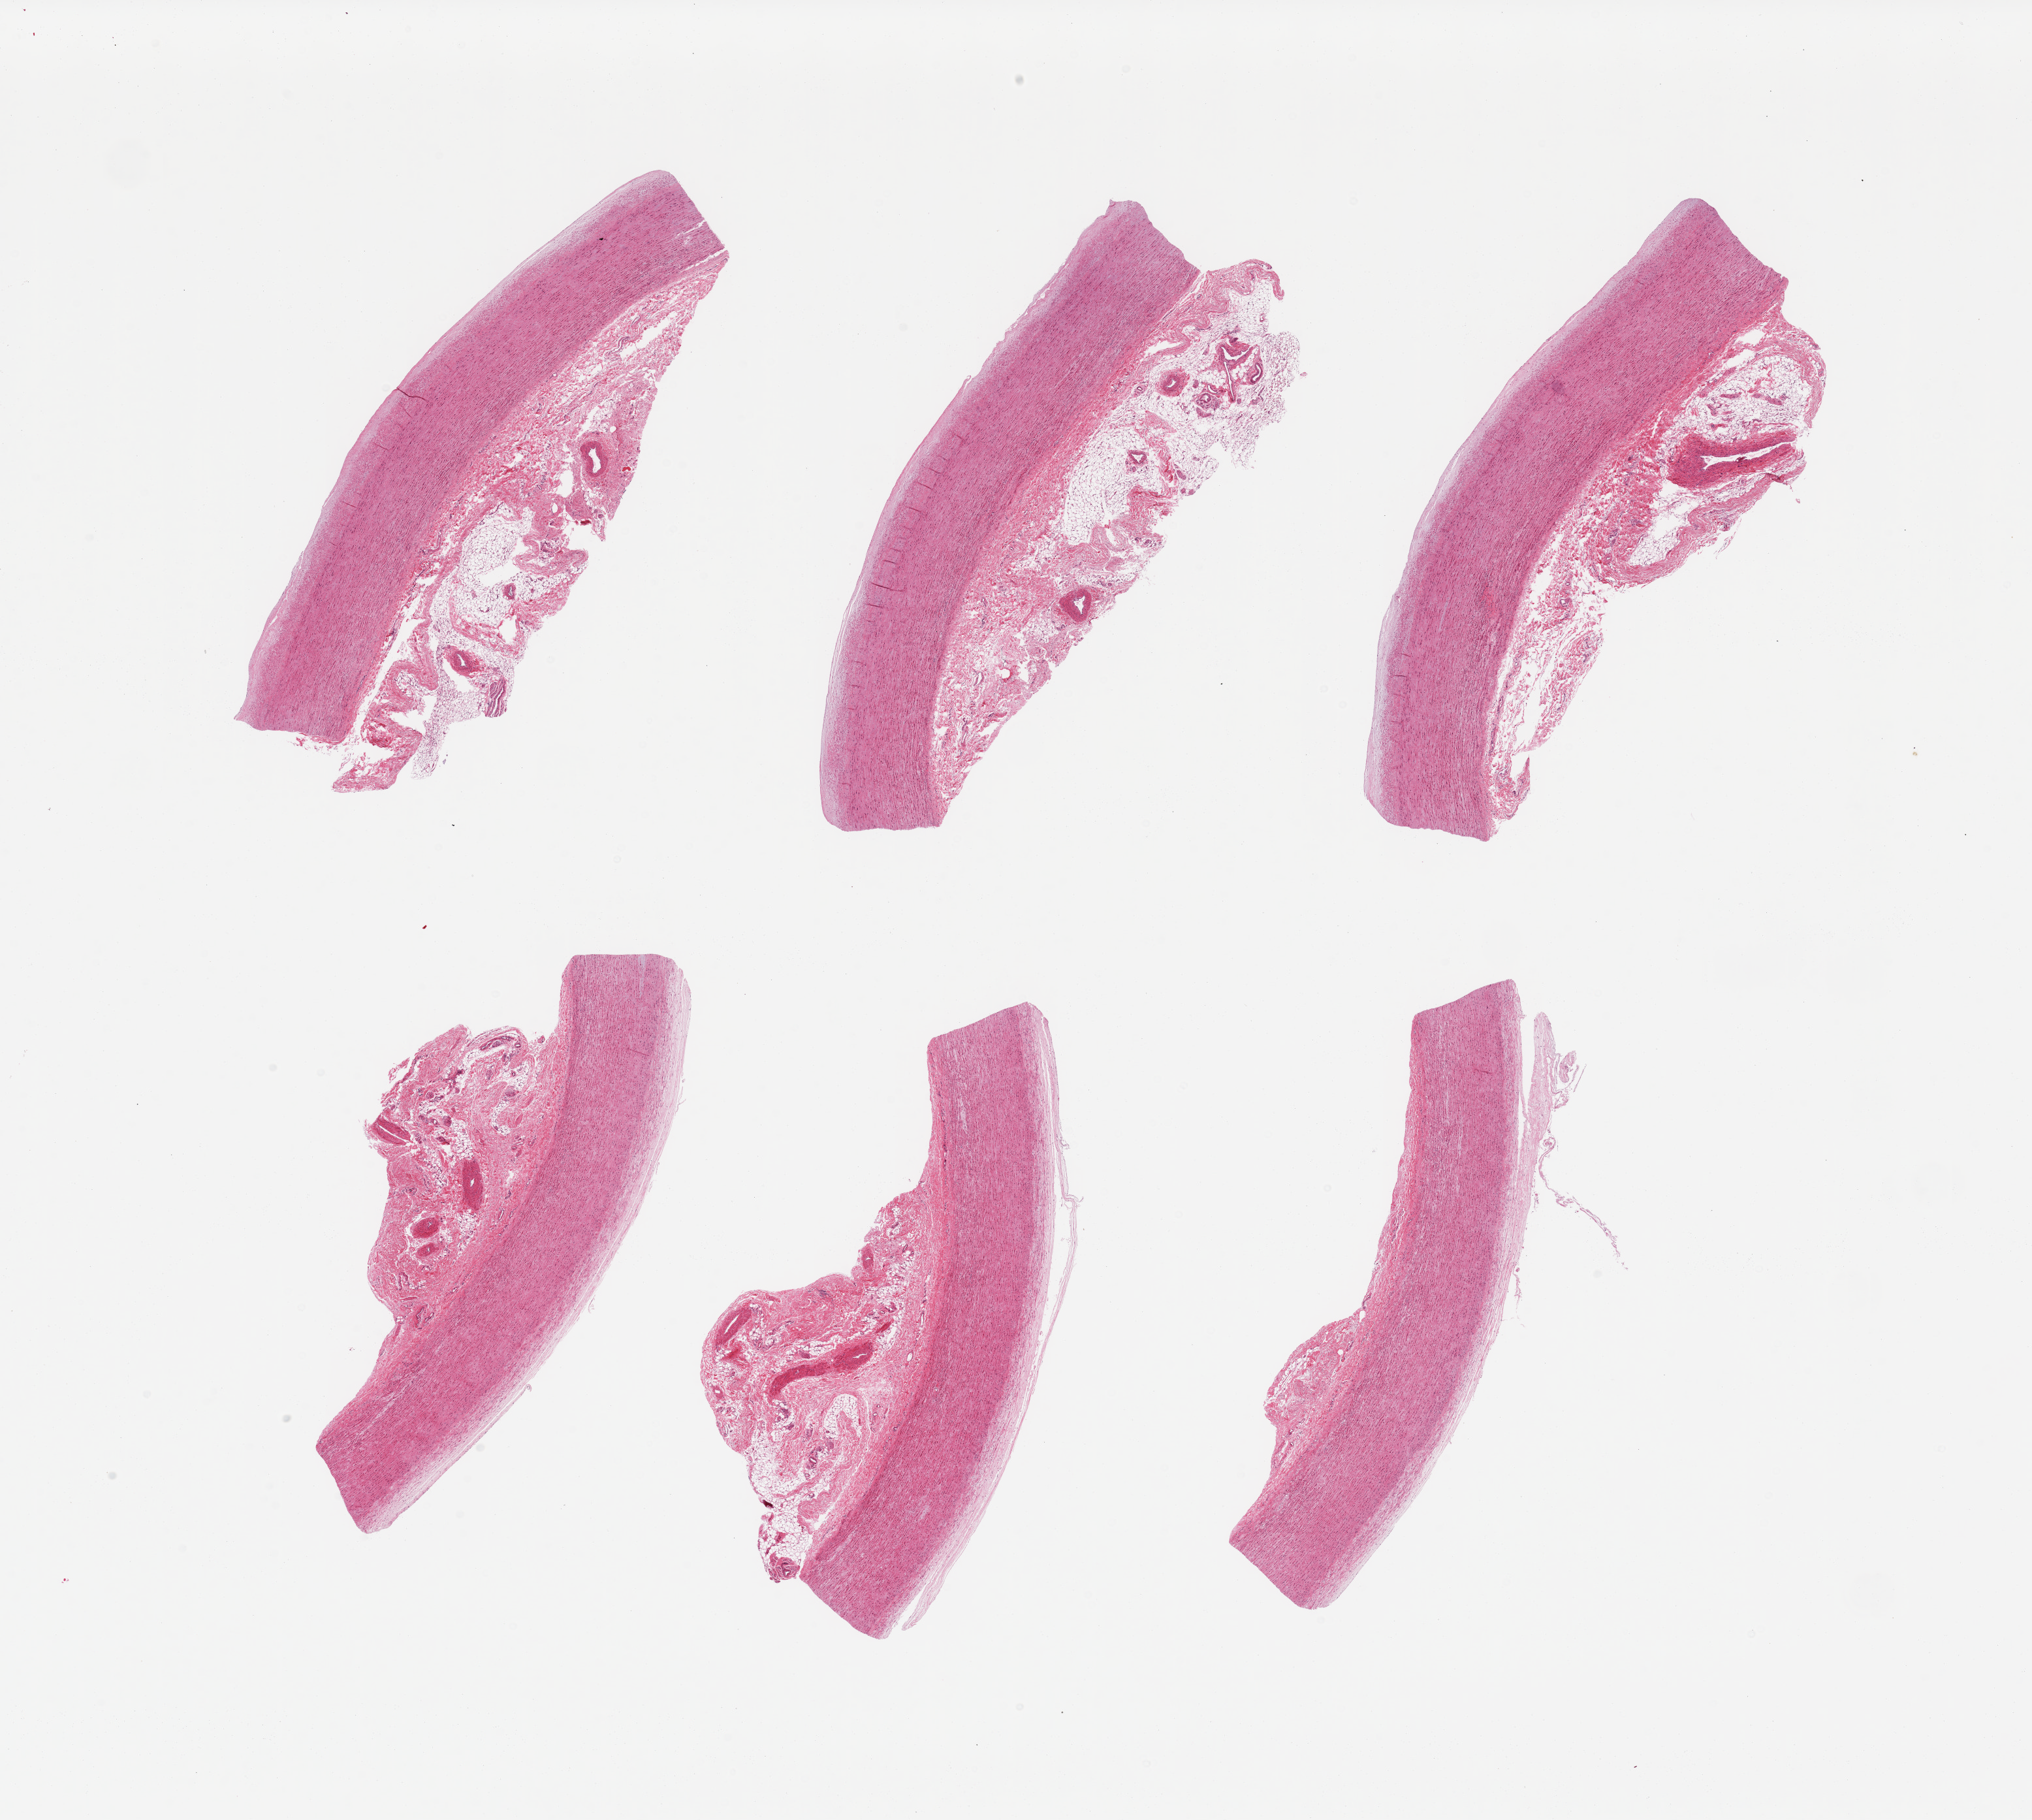
Whole-slide image, H&E stain, shown as a low-resolution overview of the whole scanned area (about 24.6 x 22.0 mm, slide scanned at 20x). PAXgene-fixed, paraffin-embedded tissue. Target tissue: aorta. Donor tissue sample. Donor sex: male.
Reviewer comment on this tissue sample: 6 pieces; early atherosis; up to 2.6mm attached adventitia with fat.